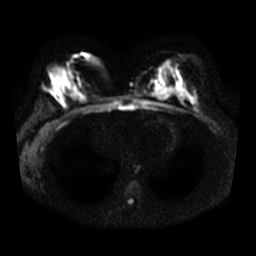
Breast MRI, one axial slice. Position 18 of 36 along the scan axis. Diffusion-weighted series; image 2 of 4 stored at this slice position (different b-values; order by instance number). 3 T. 256 × 256 image matrix. Female patient.
Structures marked on this image (outlined manually by an expert reader):
- tumour on diffusion-weighted imaging: bounding box [x1, y1, x2, y2] px = [194, 105, 199, 110]